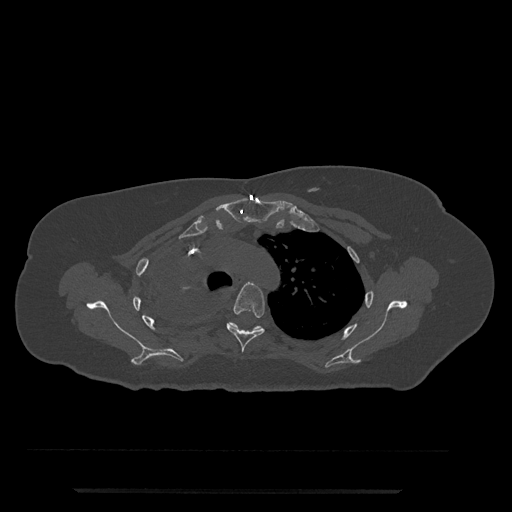
CT including the spine, one axial slice. Position 583 of 797 along the scan axis. 120 kVp. Bone window (W 1800 / L 400 HU). 0.5 mm slice thickness. 512 × 512 image matrix, field of view 440 × 440 mm. Female patient, age 51 years. From the clinical record (not read from this slice): primary cancer: neuro; vertebrae with lytic lesions (as recorded): T8.
Outlined on this slice (semi-automatic segmentation, software-assisted and operator-edited):
- T4 vertebra: bounding box <226,282,265,353> (left, top, right, bottom; pixels)
- T5 vertebra: <227,322,265,332>